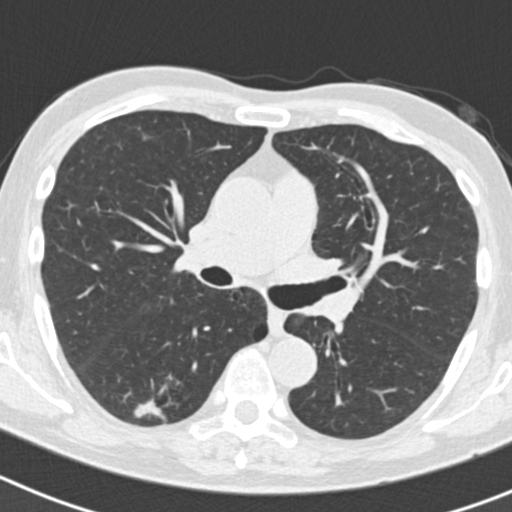
Chest CT (low-dose screening protocol), one axial image, second screening round (one year after baseline), lung window (W 1500 / L -600 HU), 2 mm slice thickness, slice 73 of 186 in the series. Male participant, aged 70 years at enrolment.
Expert reader's lesion annotation, bounding box [x1, y1, x2, y2] px = [134, 378, 196, 434]. The screening reader recorded 5 non-calcified nodules or masses ≥4 mm on this exam (right lower lobe, right lower lobe, right upper lobe, right upper lobe, left upper lobe); which of them this box marks is not recorded. Participant outcome: lung cancer diagnosed 622 days after this screen (after the third annual screen) — bronchiolo-alveolar adenocarcinoma, NOS, right lower lobe, poorly differentiated (G3), stage IB (AJCC 6th edition), 30 mm at pathology.